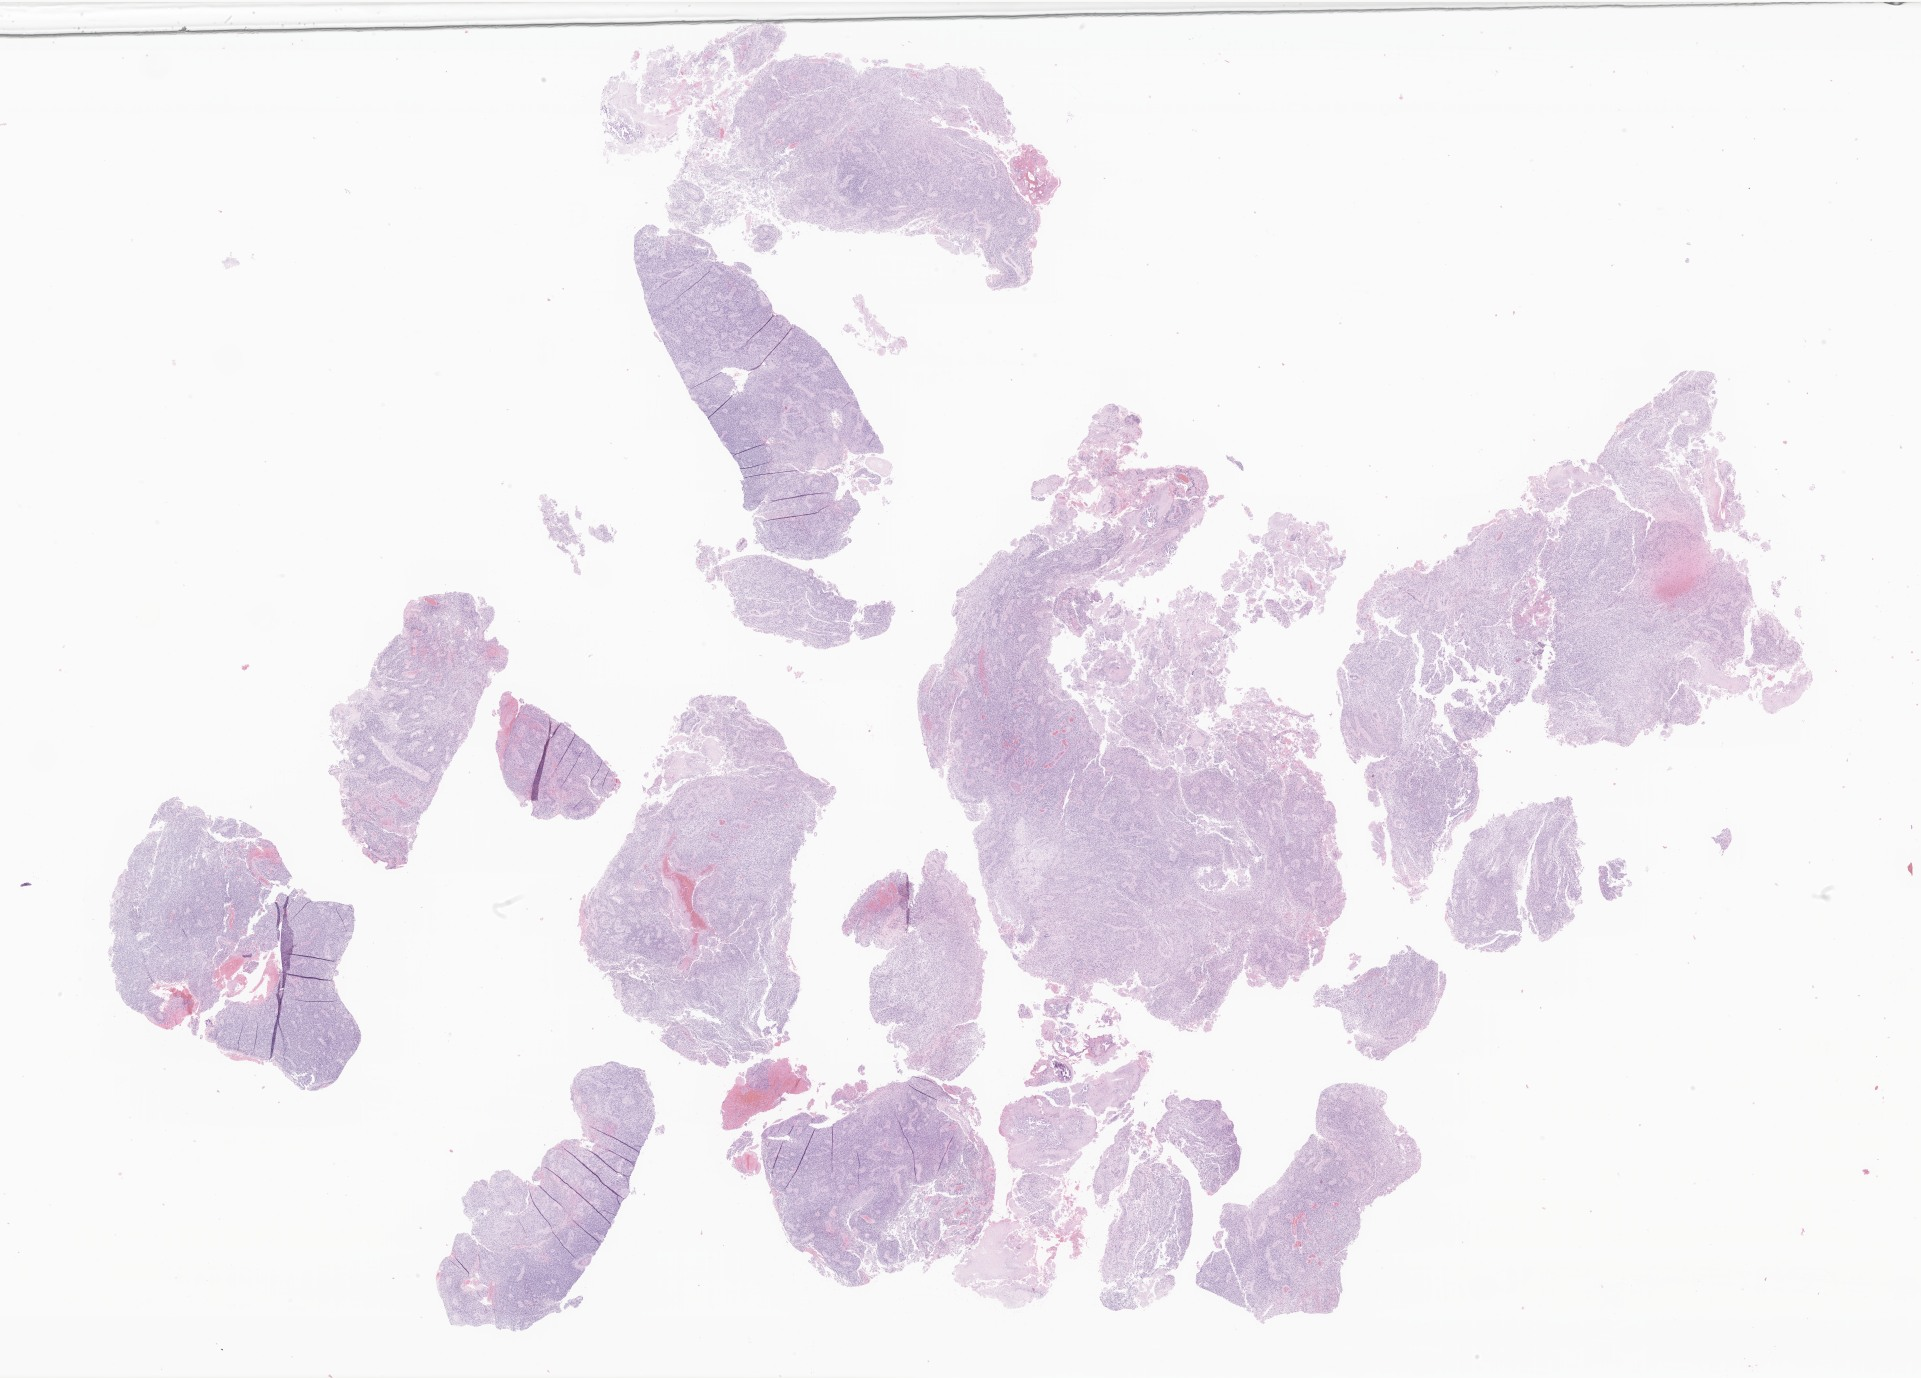
Whole-slide image, H&E stain of tumor tissue from the brain, a low-resolution overview of the entire scanned area, about 32.4 x 23.2 mm. FFPE section. Patient female; age 227 days.
- recorded diagnosis: Ependymoma, NOS